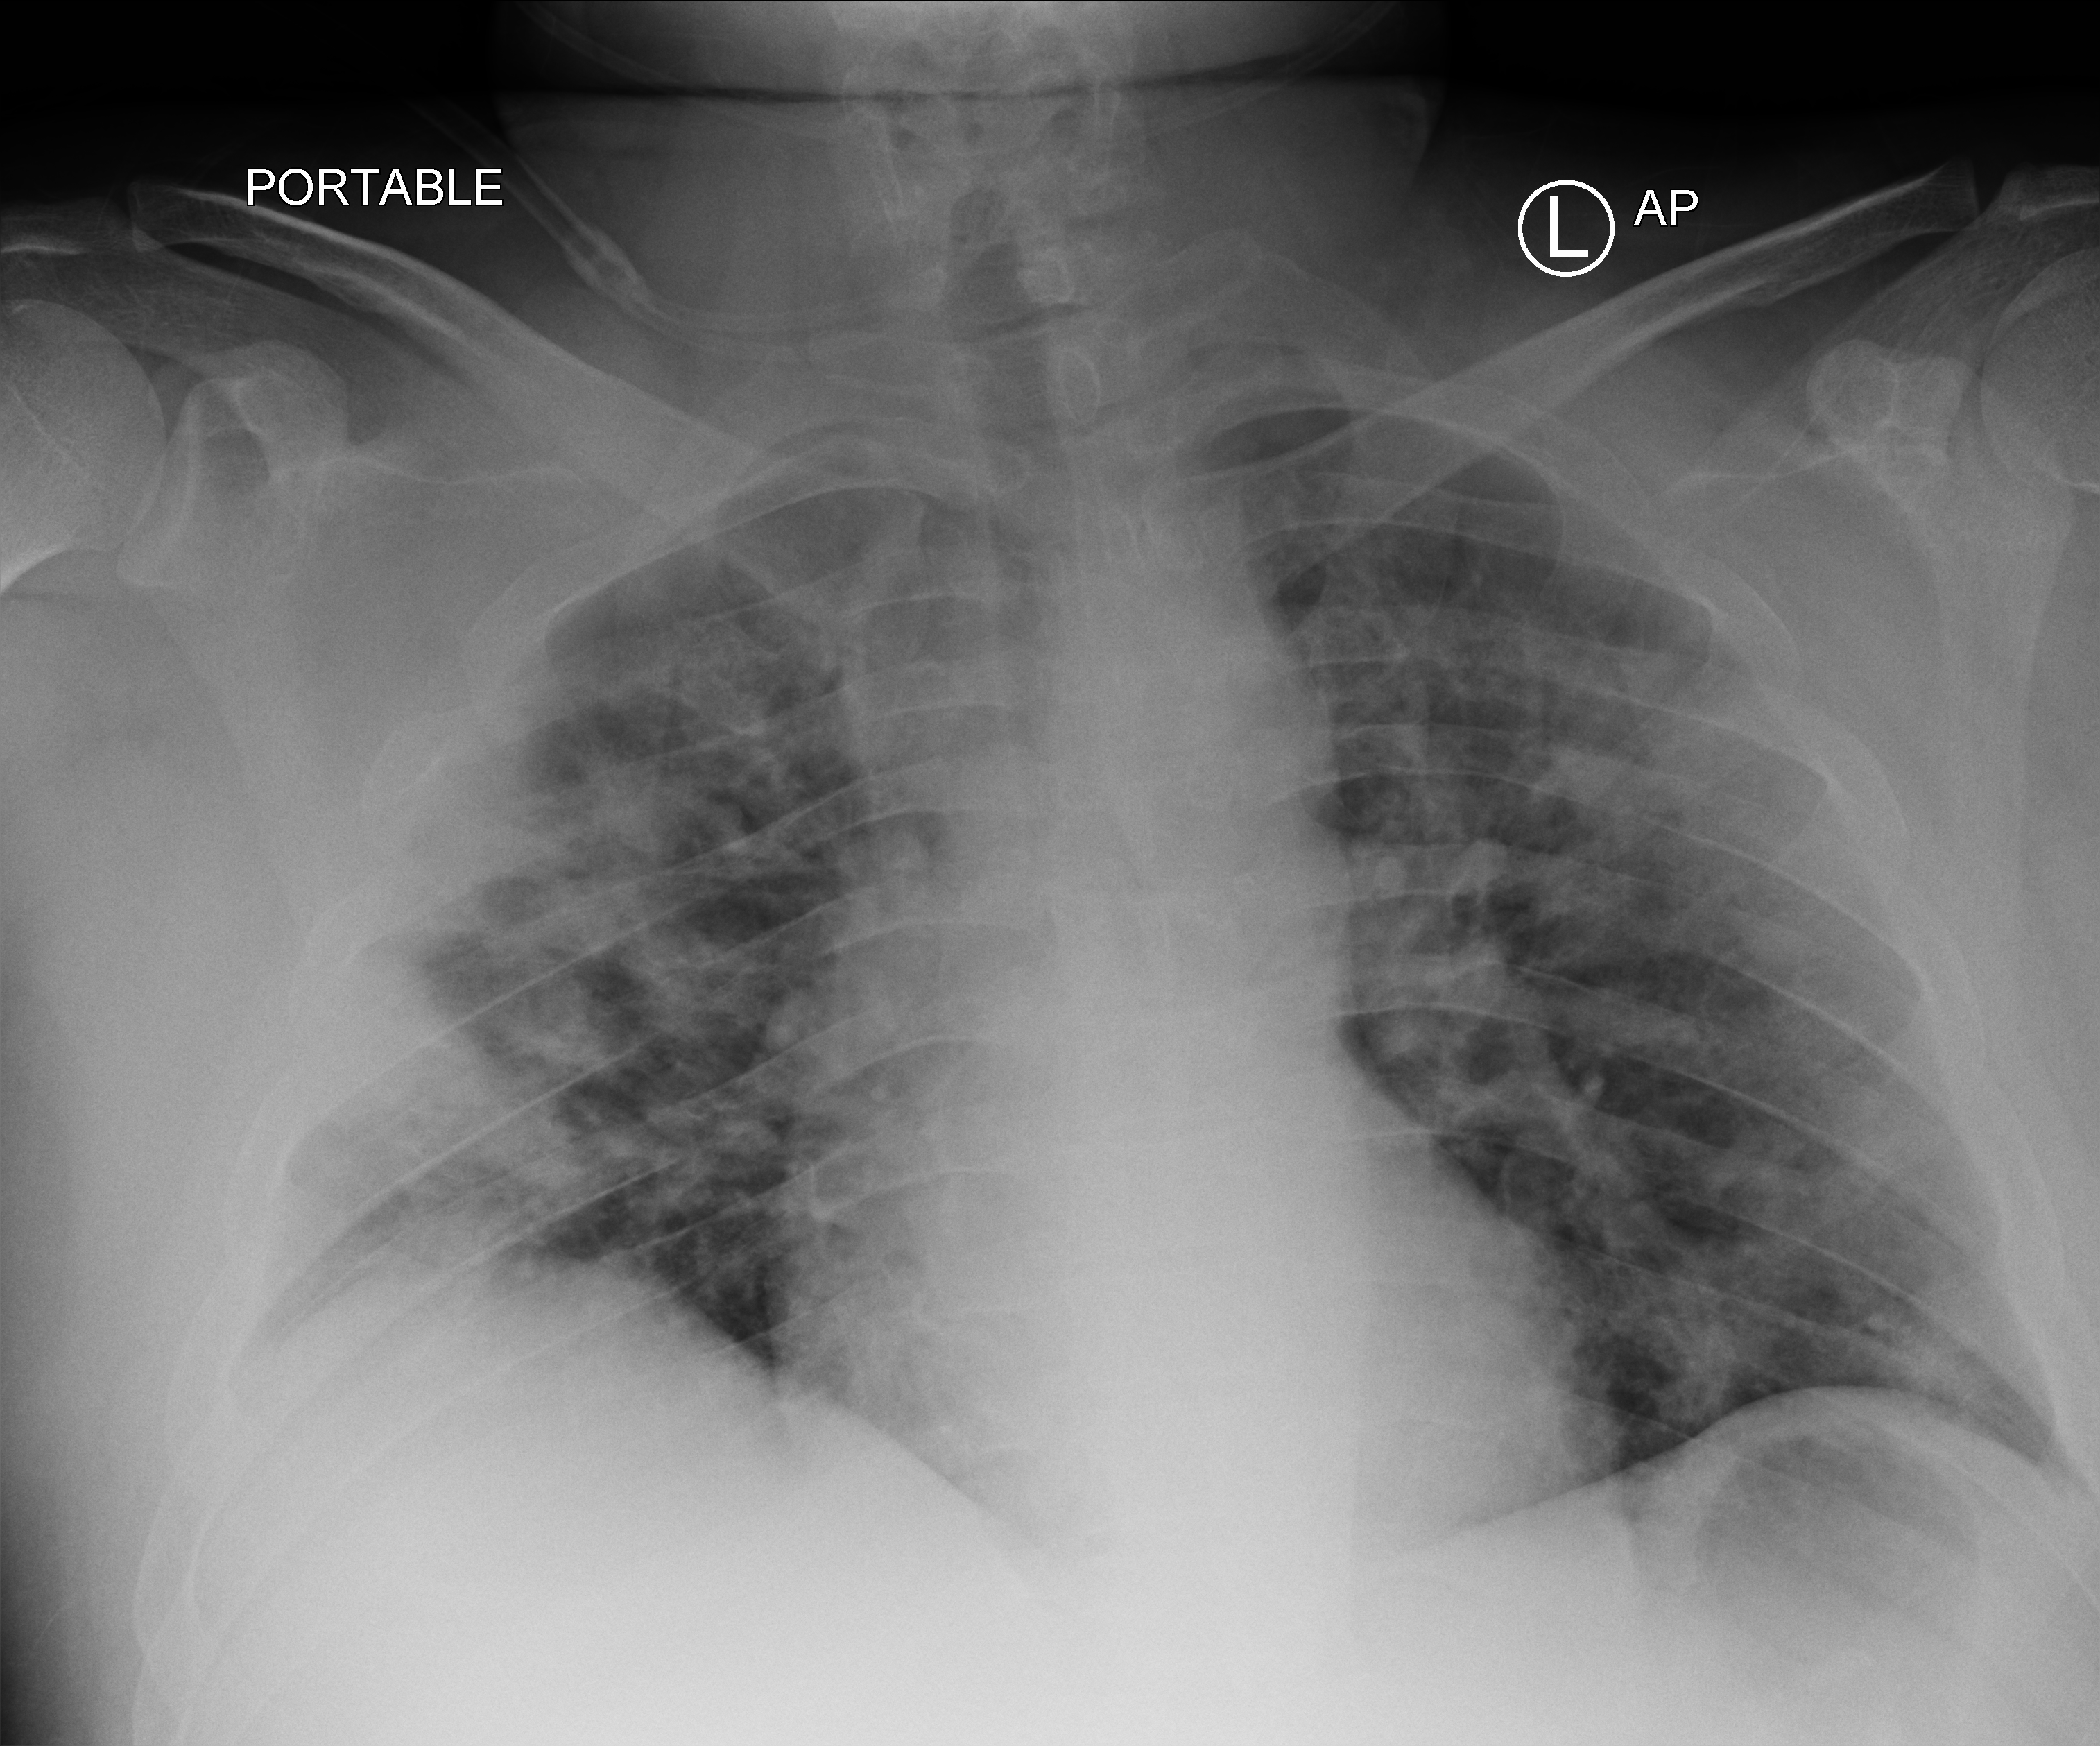
Chest X-ray (portable), anteroposterior (AP) projection. Female patient hospitalised with COVID-19, age 18–59 years.
Admission-level facts for this patient (not findings on this image; timing relative to this image not recorded):
- mechanically ventilated during this hospital stay: yes